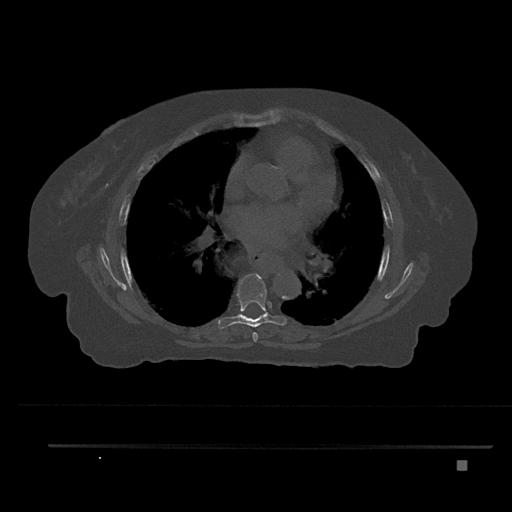
CT including the spine, one axial slice. Slice 491 of 797 in the series (ordered by position). Bone window (W 1800 / L 400 HU). 512 × 512 image matrix. Female patient, age 76 years. From the clinical record (not read from this slice): primary cancer: lung; vertebrae with lytic lesions (as recorded): T11, L3.
Outlined on this slice (semi-automatic segmentation, software-assisted and operator-edited):
- T6 vertebra: bounding box (x1, y1, x2, y2) in pixels: (252, 332, 258, 342)
- T7 vertebra: (218, 273, 287, 331)